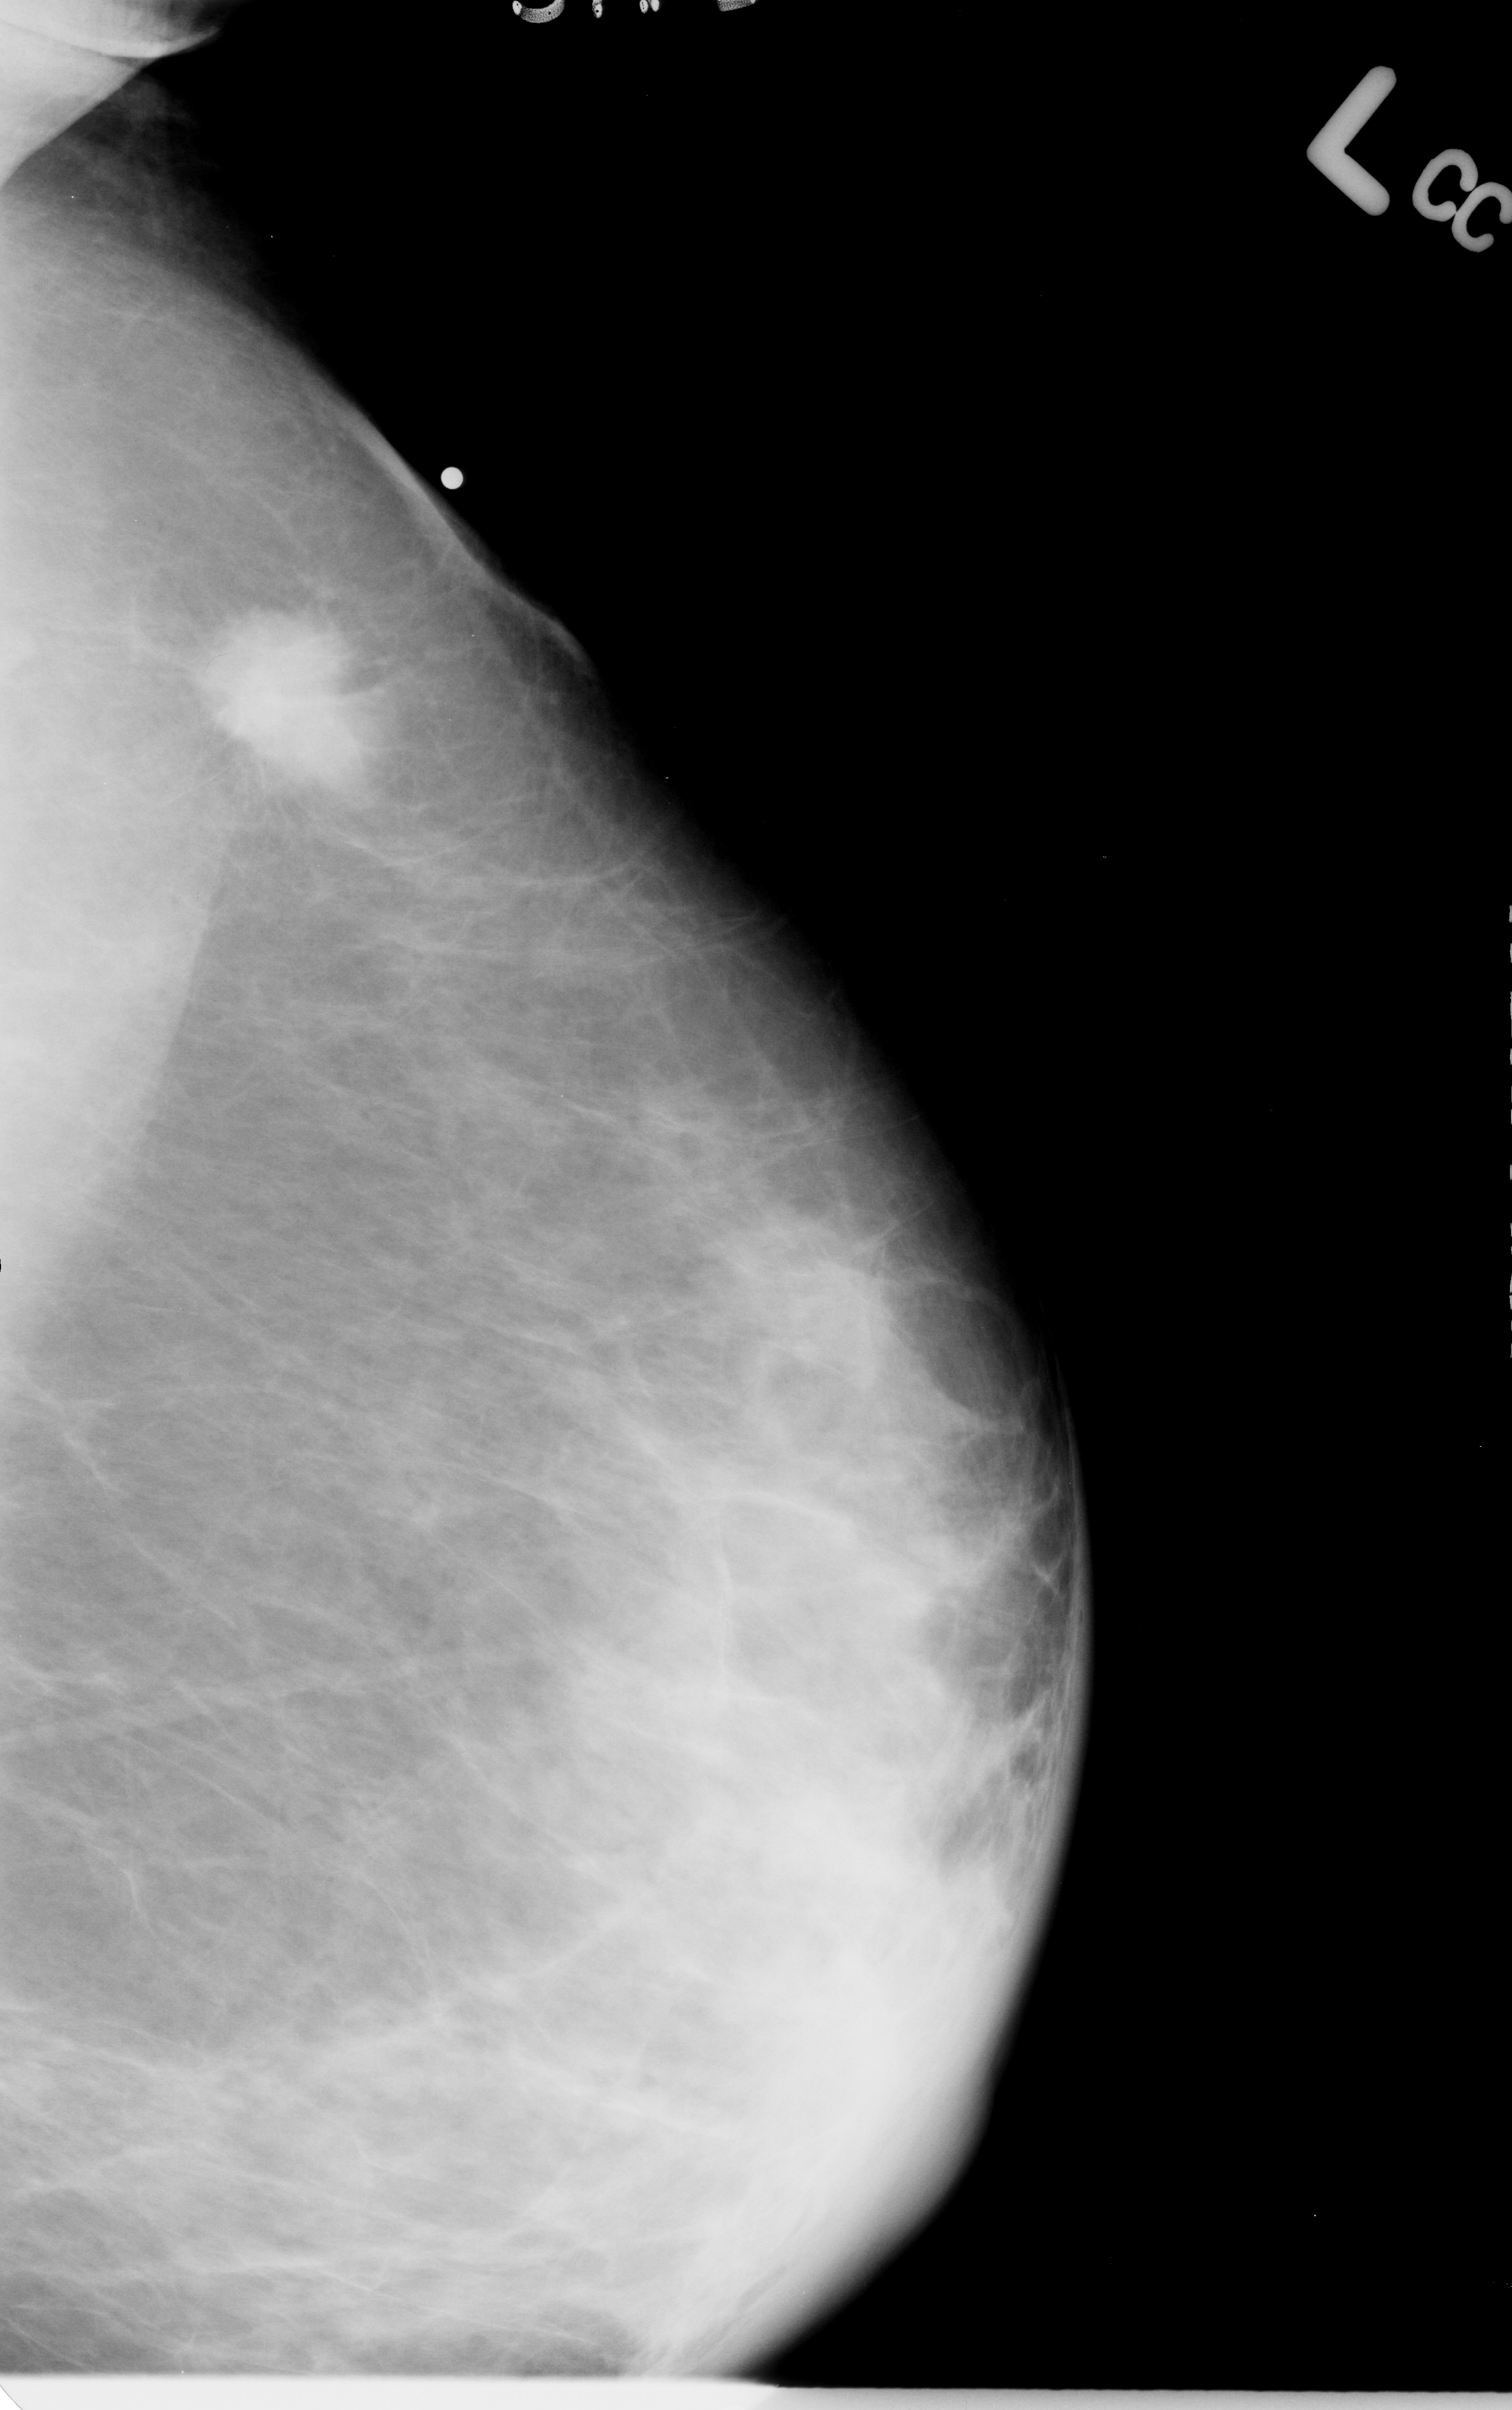
Mammogram (digitized film); left breast; MLO view.
Finding: mass, shape irregular, margins spiculated; BI-RADS assessment category 5; subtlety rating 5 on a 1 (subtle) to 5 (obvious) scale; pathology (as recorded): malignant.